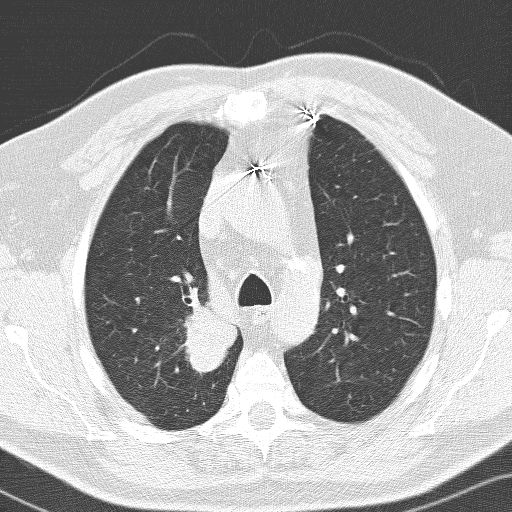
Low-dose screening chest CT, axial slice, baseline screening round, lung window (W 1500 / L -600 HU), 3.2 mm slice thickness, slice 36 of 141 in the series, 512 × 512 image matrix. Male participant, aged 66 years at enrolment. Former smoker at enrolment.
Lesion marked by an expert reader, bounding box <148,301,231,391> (left, top, right, bottom; pixels). Reader record for this screening exam (exam-level; its link to the box is not recorded): non-calcified nodule or mass ≥4 mm, right upper lobe, 36 × 30 mm, spiculated (stellate) margins, soft tissue attenuation. Official screen result: positive, change unspecified: nodule(s) >= 4 mm or enlarging nodule(s), mass(es), or other non-specific abnormalities suspicious for lung cancer. Lung cancer was diagnosed 103 days after this screen: adenocarcinoma, NOS, right upper lobe, poorly differentiated (G3), stage IIB (AJCC 6th edition), 33 mm at pathology.